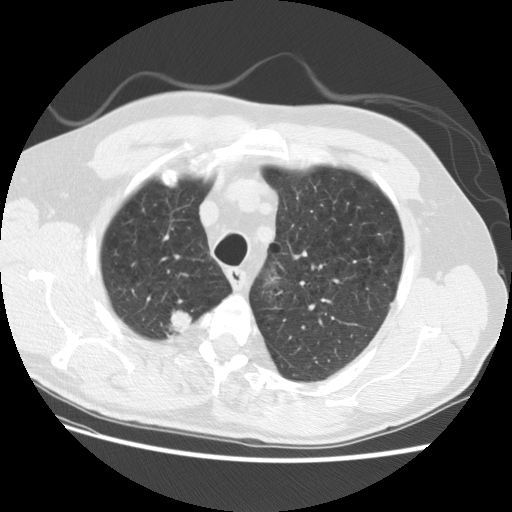
Axial slice from a low-dose chest CT screening exam, baseline screening round, lung window (W 1500 / L -600 HU), 2.5 mm slice thickness, 140 kVp. Male participant, aged 69 years at enrolment.
Expert reader's lesion annotation, bounding box [x1, y1, x2, y2] px = [158, 305, 200, 339]. The exam's reader record, not a measurement of the box and not confirmed to be the same lesion: non-calcified nodule or mass ≥4 mm, right upper lobe, 15 × 15 mm, spiculated (stellate) margins, soft tissue attenuation. Later outcome: lung cancer diagnosed 22 days after this screen — large cell neuroendocrine carcinoma, right upper lobe, poorly differentiated (G3), stage IA (AJCC 6th edition), 23 mm at pathology.